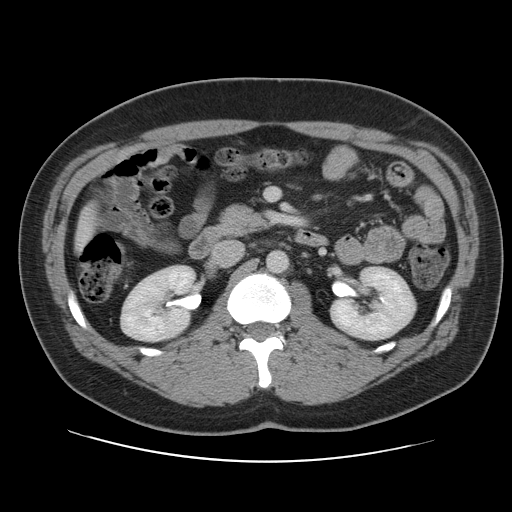
Contrast-enhanced abdominal CT, one axial slice. Slice 45 of 109 in the series (ordered by position). Intravenous contrast given. Soft-tissue window (W 400 / L 40 HU). 5 mm slice thickness. 512 × 512 image matrix, field of view 402 × 402 mm. Male patient, age 35 years. From the clinical record (not read from this slice): diagnosis: colorectal cancer liver metastases, imaged before liver resection; multiple liver metastases: yes; largest metastasis: 2.8 cm; chemotherapy before resection: yes.
Outlined on this slice (expert manual segmentation):
- liver: box from (x=76, y=208) to (x=97, y=246) px
- planned liver remnant (the part of the liver to remain after resection): (x=76, y=208)–(x=97, y=246)